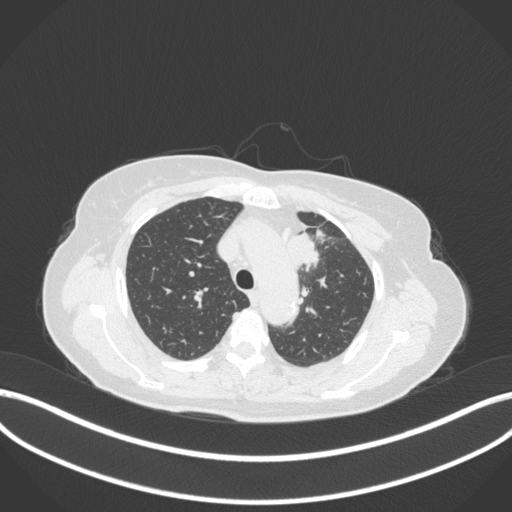
Chest CT, one axial slice; position 251 of 368 along the scan axis; reconstruction kernel B31f; 120 kVp; lung window (W 1500 / L -600 HU); 1 mm slice thickness; 512 × 512 image matrix, field of view 400 × 400 mm. Female patient, age 65 years. From the clinical record (not read from this slice): clinical TNM (as recorded): T2a N0 M0; histopathological grade: G2-3.
Annotated regions visible in this slice (rectangle marked by the reading radiologist):
- lung tumour (recorded histology: adenocarcinoma): bounding box (x1, y1, x2, y2) in pixels: (286, 229, 320, 274)